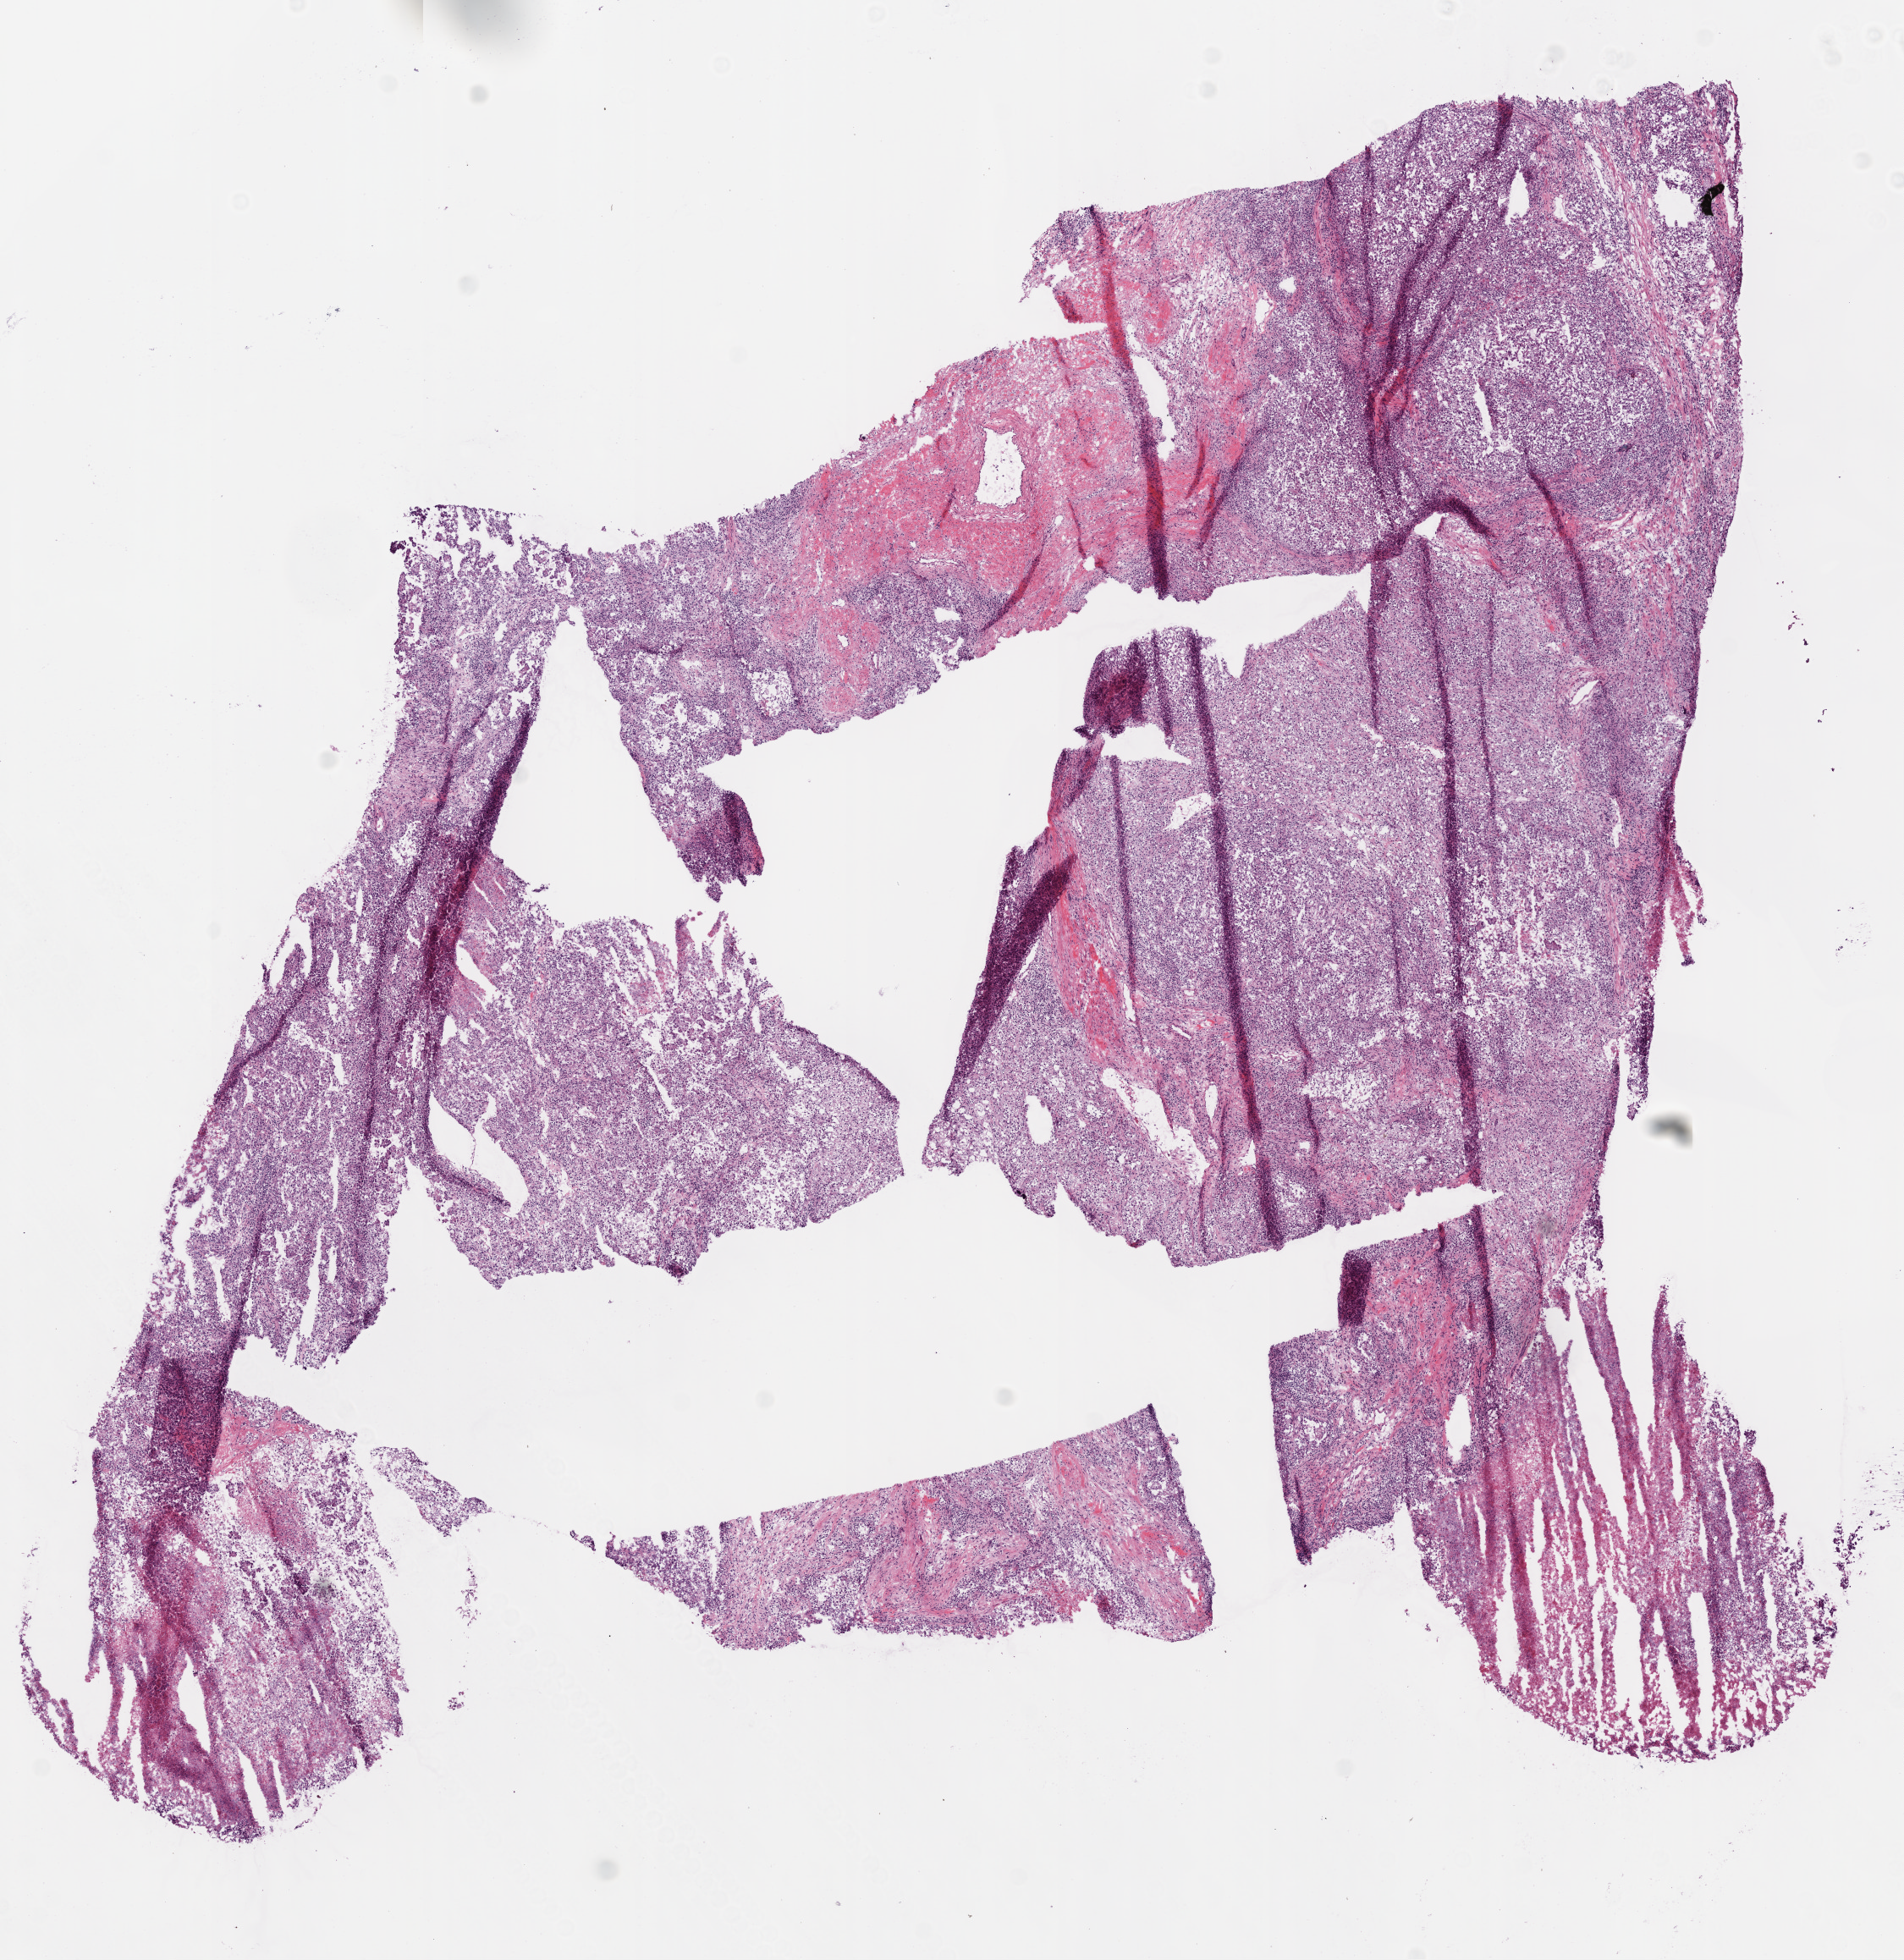
Digitized H&E tissue section (whole slide), a low-resolution overview of the entire scanned area, about 9.0 x 9.3 mm (acquisition: 20x scan). Frozen section from the bottom of the tissue portion. Sample: primary tumour, kidney. Patient: male, age at initial diagnosis 37 years. Histologic grade: G3 (poorly differentiated). Composition of this section per pathologist review: tumour cells 80%, tumour nuclei 75%, normal cells 0%, stromal cells 10%, necrosis 10%.
- AJCC pathologic stage: III
- TNM: T3a N1 M0
- histologic diagnosis: Clear cell adenocarcinoma, NOS